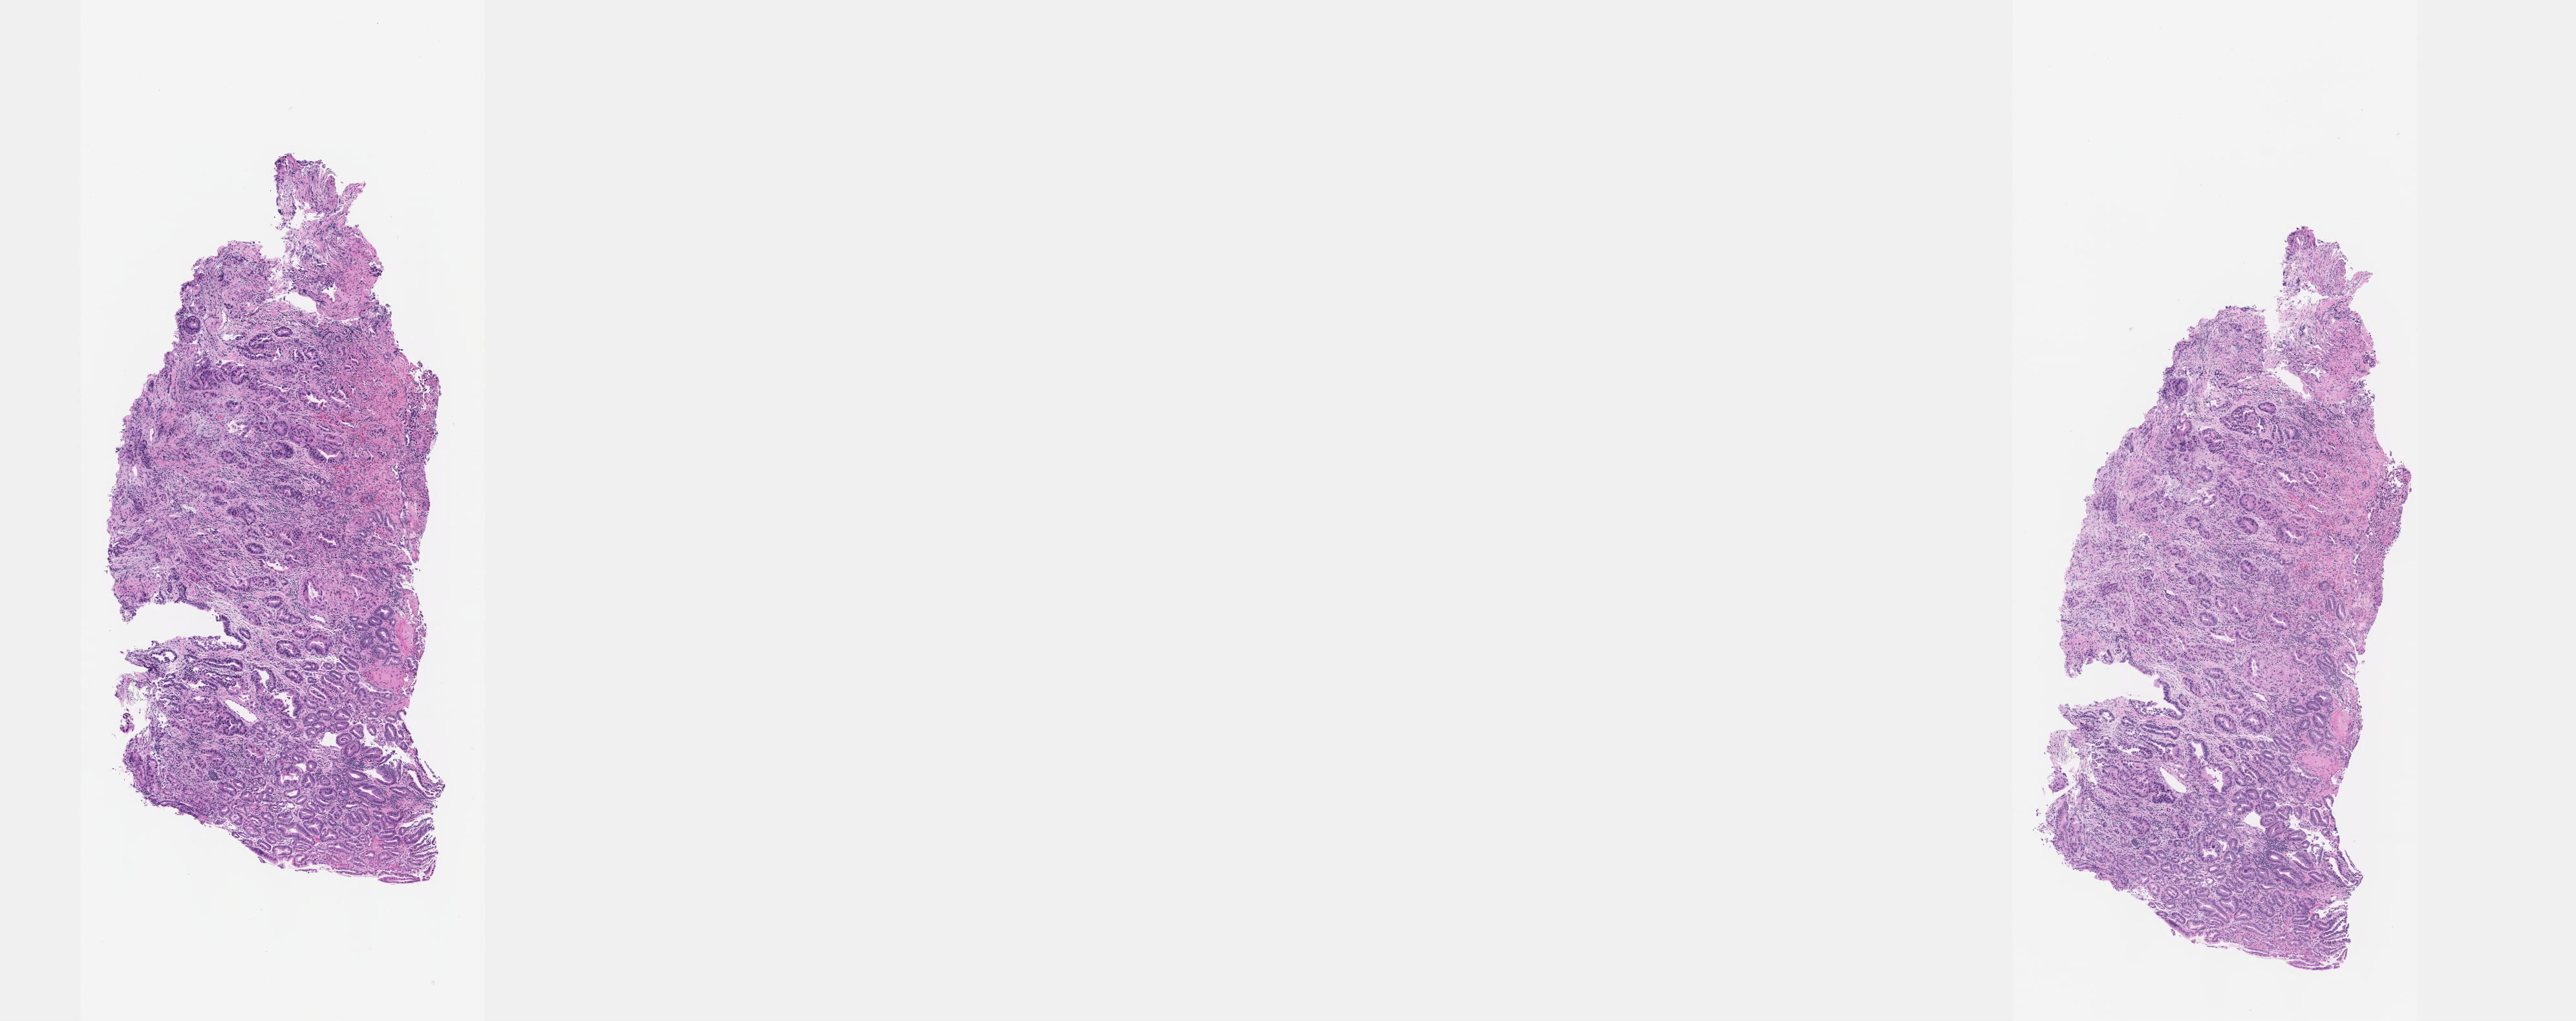
Whole-slide histology image, H&E-stained, low-resolution overview of the scanned area, about 16.1 x 6.4 mm (slide scanned at 40x). Formalin-fixed paraffin-embedded (FFPE) diagnostic section. Primary tumour sample from the stomach. Patient: male, age at initial diagnosis 51 years. Slide review estimates, as recorded: tumour cells 63%, tumour nuclei 77%.
Histologic diagnosis: Tubular adenocarcinoma (cardia, NOS).